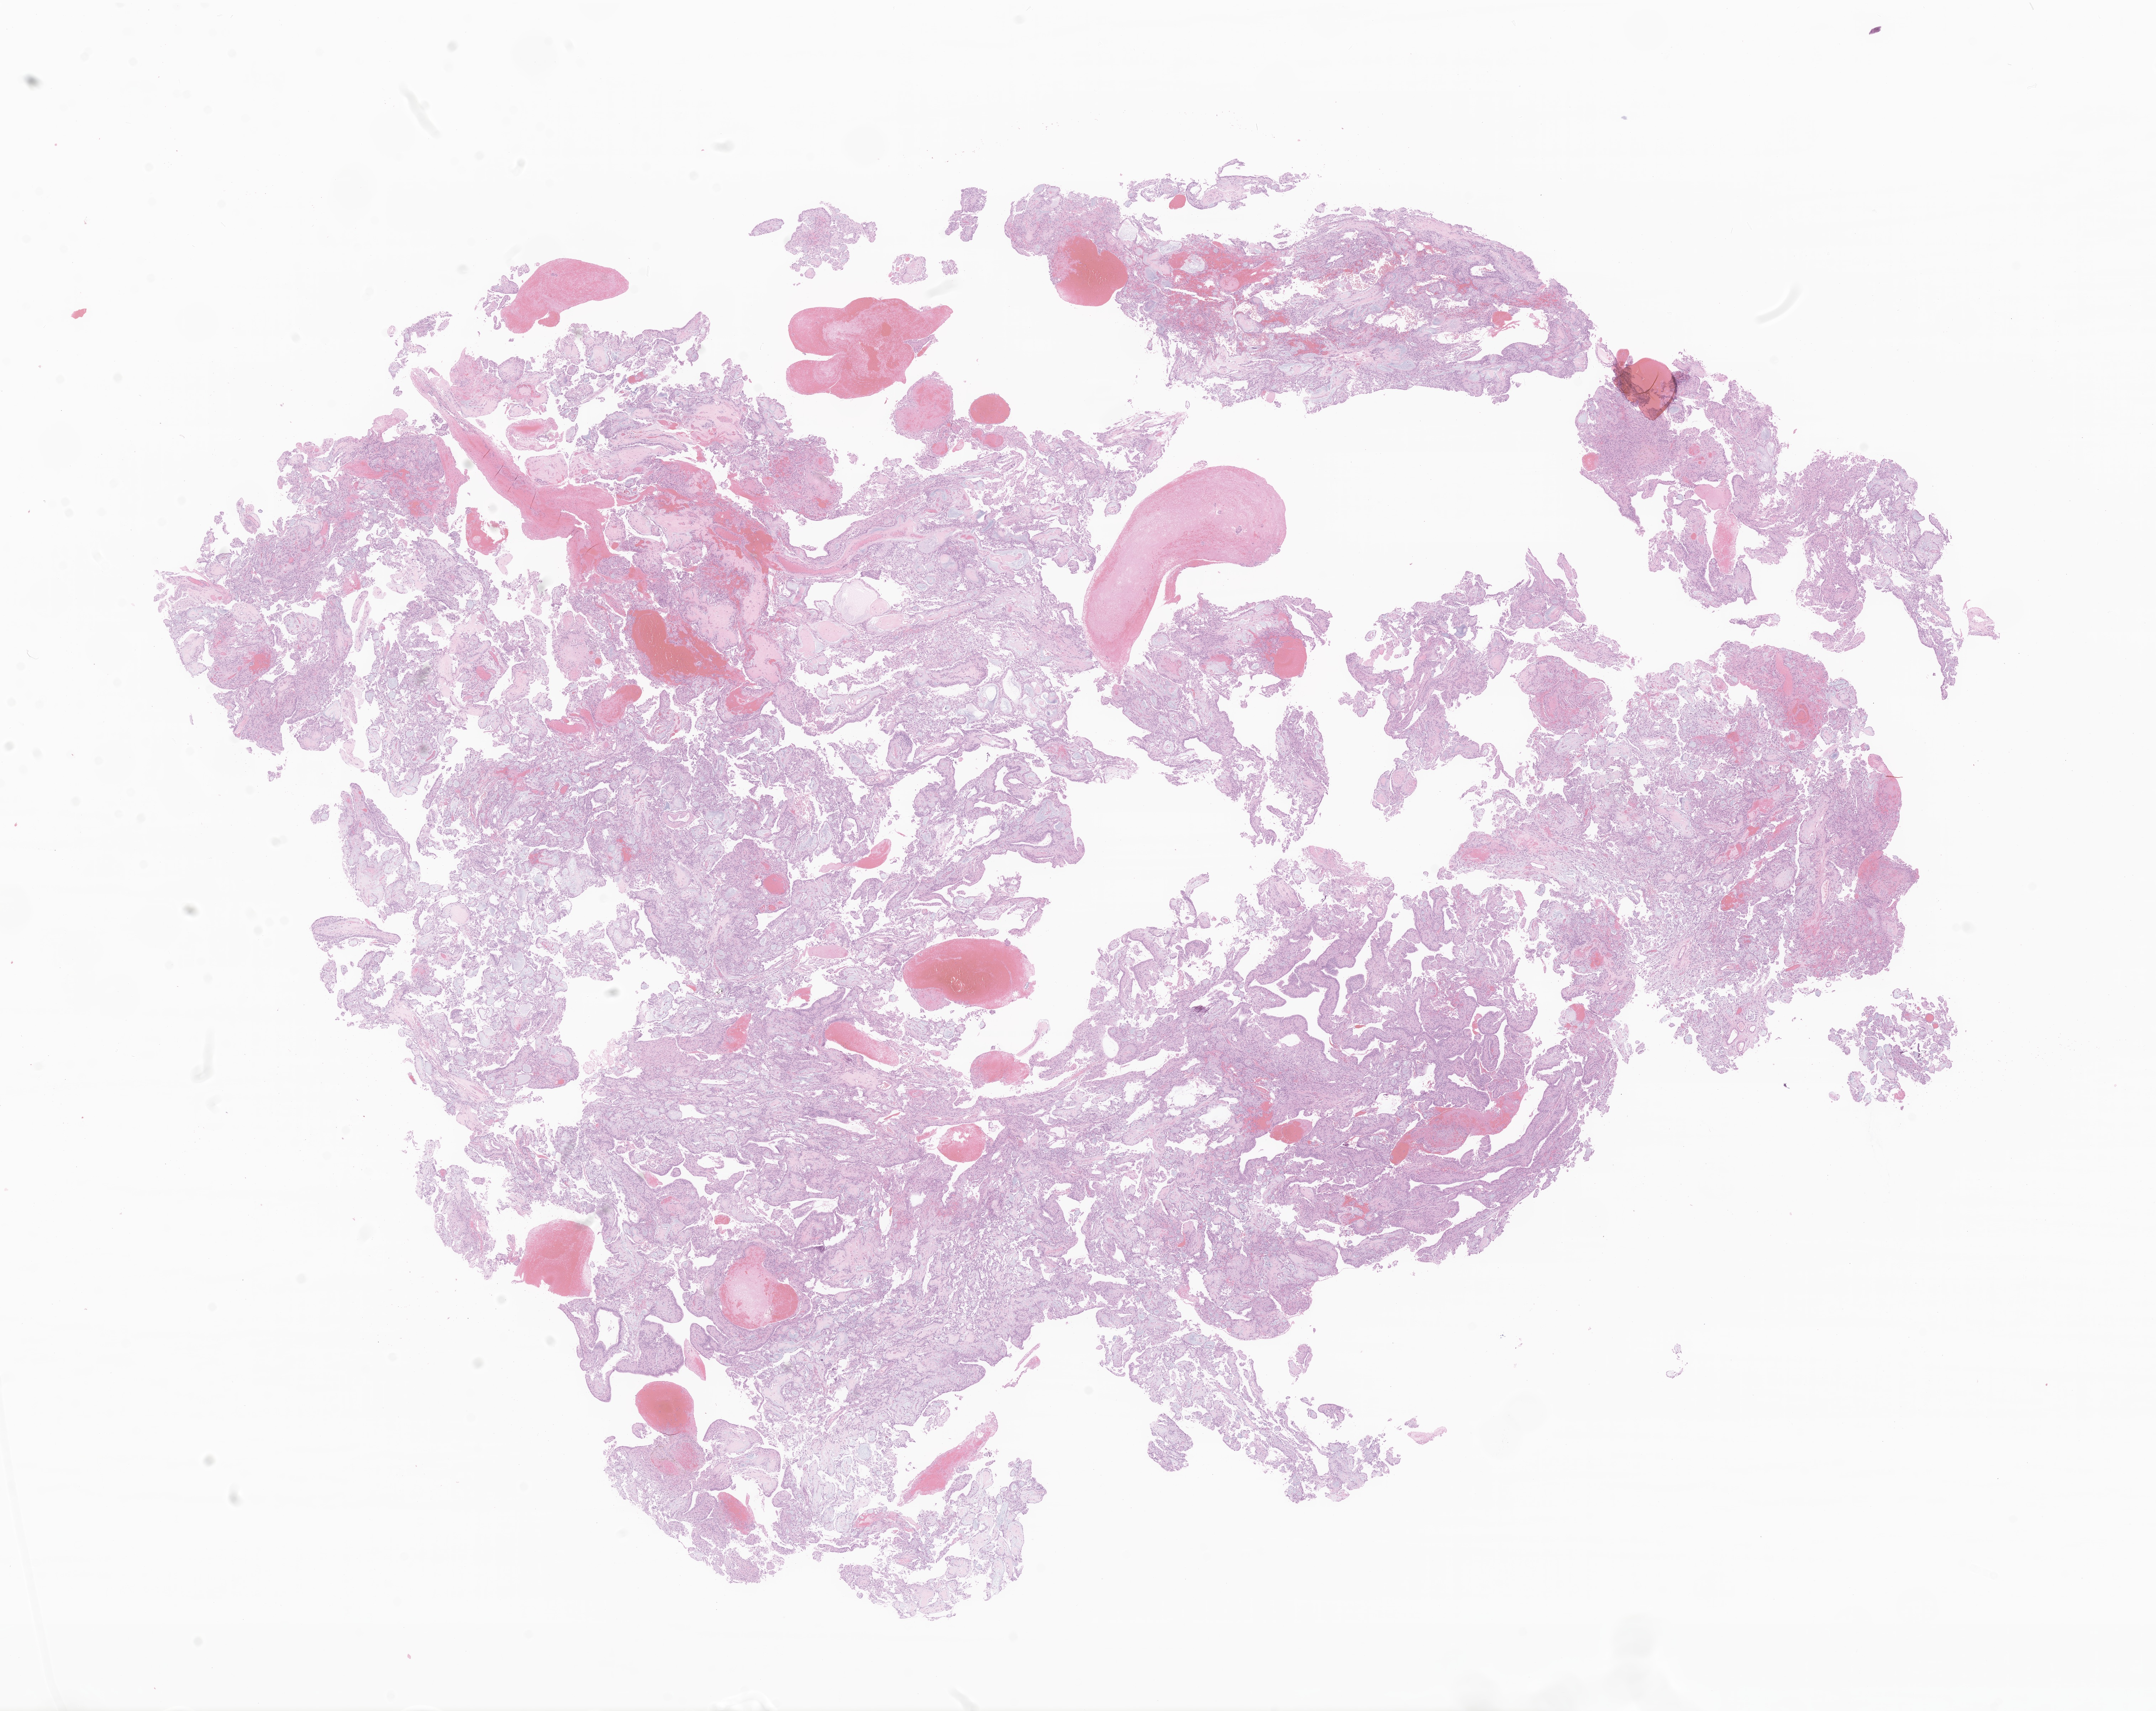
Whole-slide image, H&E stain of tumor tissue from the spinal cord, a low-resolution overview of the entire scanned area, about 25.5 x 20.3 mm; formalin-fixed, paraffin-embedded (FFPE) tissue. Patient female; age 181 months.
Diagnosis (ICD-O-3 morphology term): Myxopapillary ependymoma.